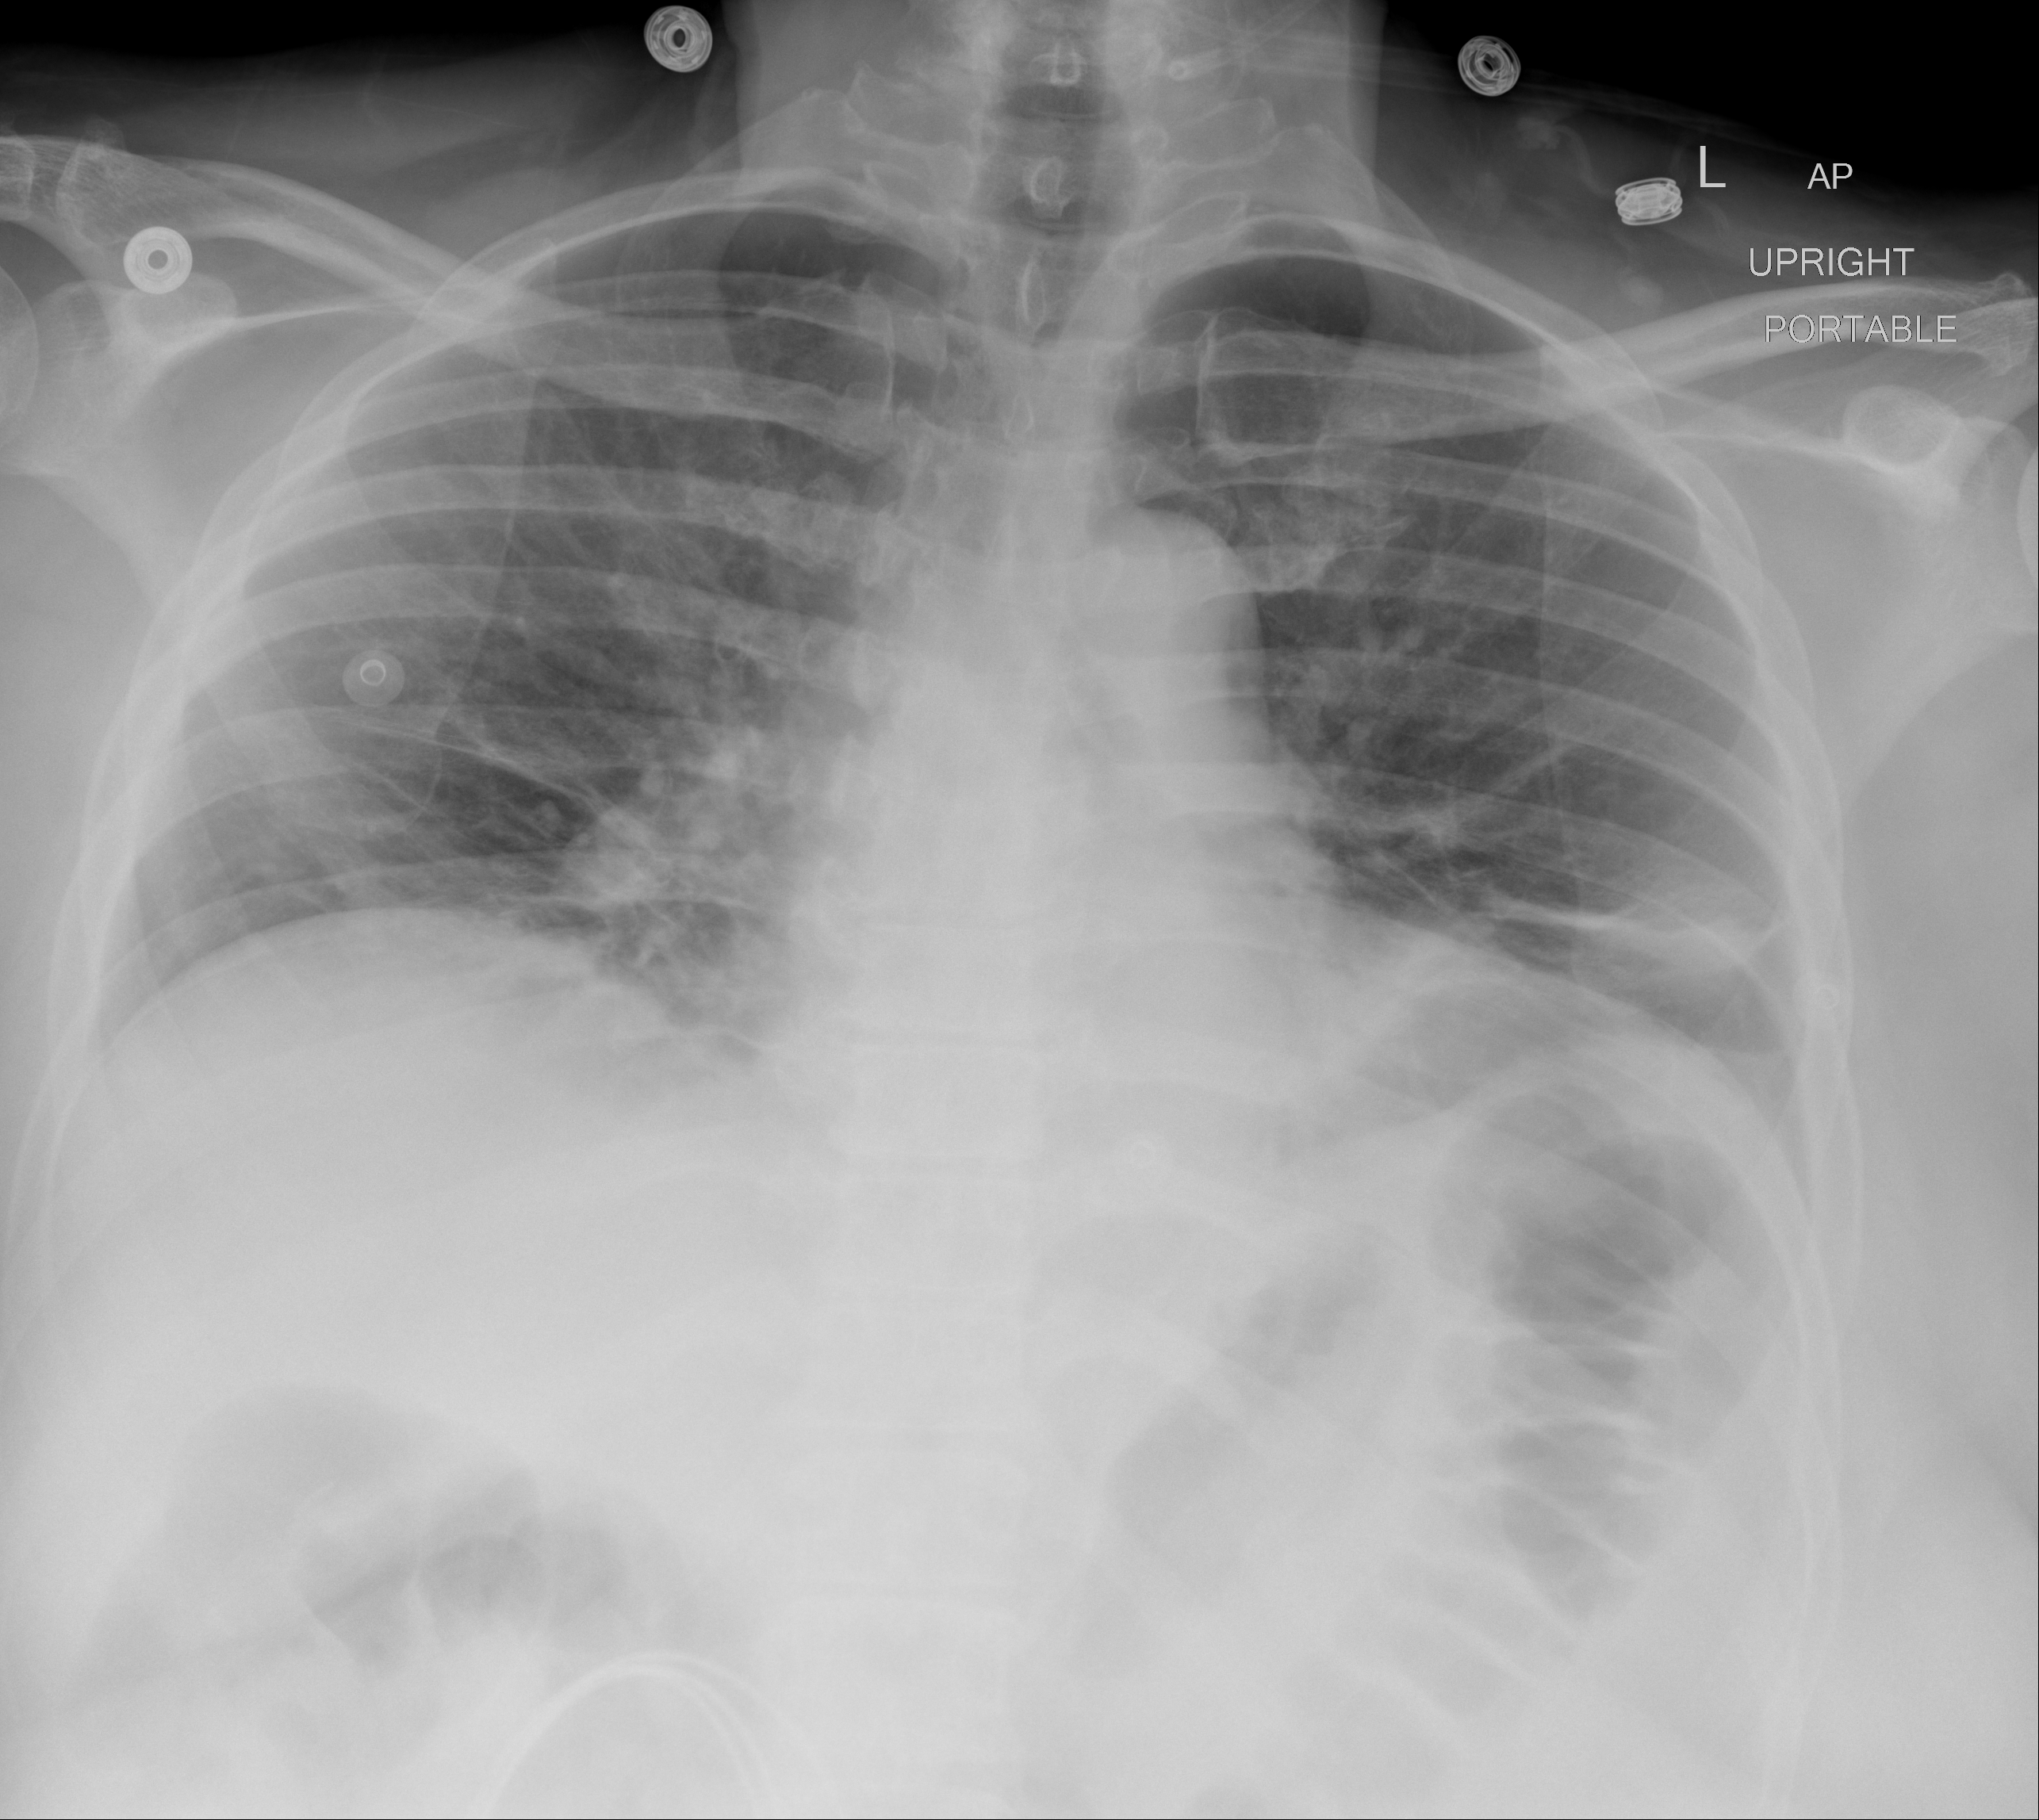
Portable chest radiograph, AP projection. Female patient, age 57 years; COVID-19 (test-positive).
Radiologist's key findings for this exam: mild bibasilar airspace disease is not significantly changed from prior.